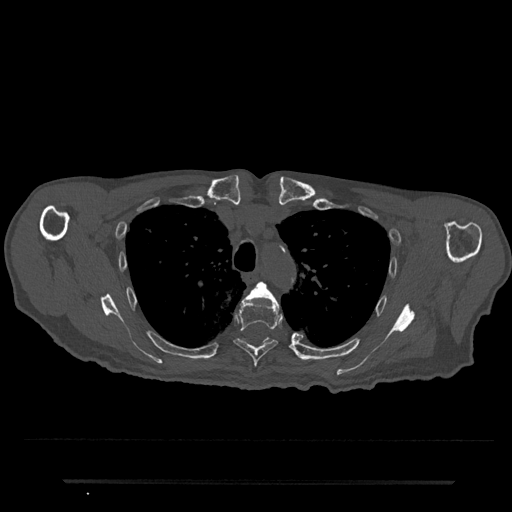
CT including the spine, one axial slice. Slice 580 of 797 in the series (ordered by position). 120 kVp. Bone window (W 1800 / L 400 HU). 0.5 mm slice thickness. 512 × 512 image matrix. Male patient, age 74 years. From the clinical record (not read from this slice): primary cancer: prostate.
Annotated regions visible in this slice (semi-automatic segmentation, software-assisted and operator-edited):
- T4 vertebra: bounding box <246,282,276,300> (left, top, right, bottom; pixels)
- T5 vertebra: <234,295,282,367>
- T6 vertebra: <243,338,270,344>